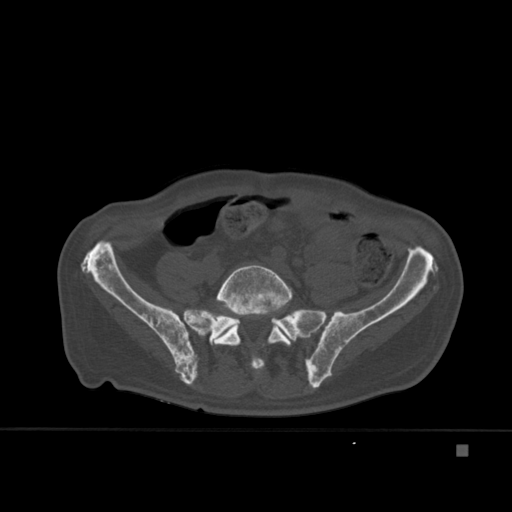
CT including the spine, one axial slice; bone window (W 1800 / L 400 HU); 1.5 mm slice thickness; 512 × 512 image matrix, field of view 378 × 378 mm. Patient: male, 75 years. From the clinical record (not read from this slice): primary cancer: prostate.
Annotated regions visible in this slice (semi-automatic segmentation, software-assisted and operator-edited):
- L5 vertebra: box from (x=211, y=265) to (x=293, y=369) px
- T7 vertebra: (x=237, y=324)–(x=239, y=328)